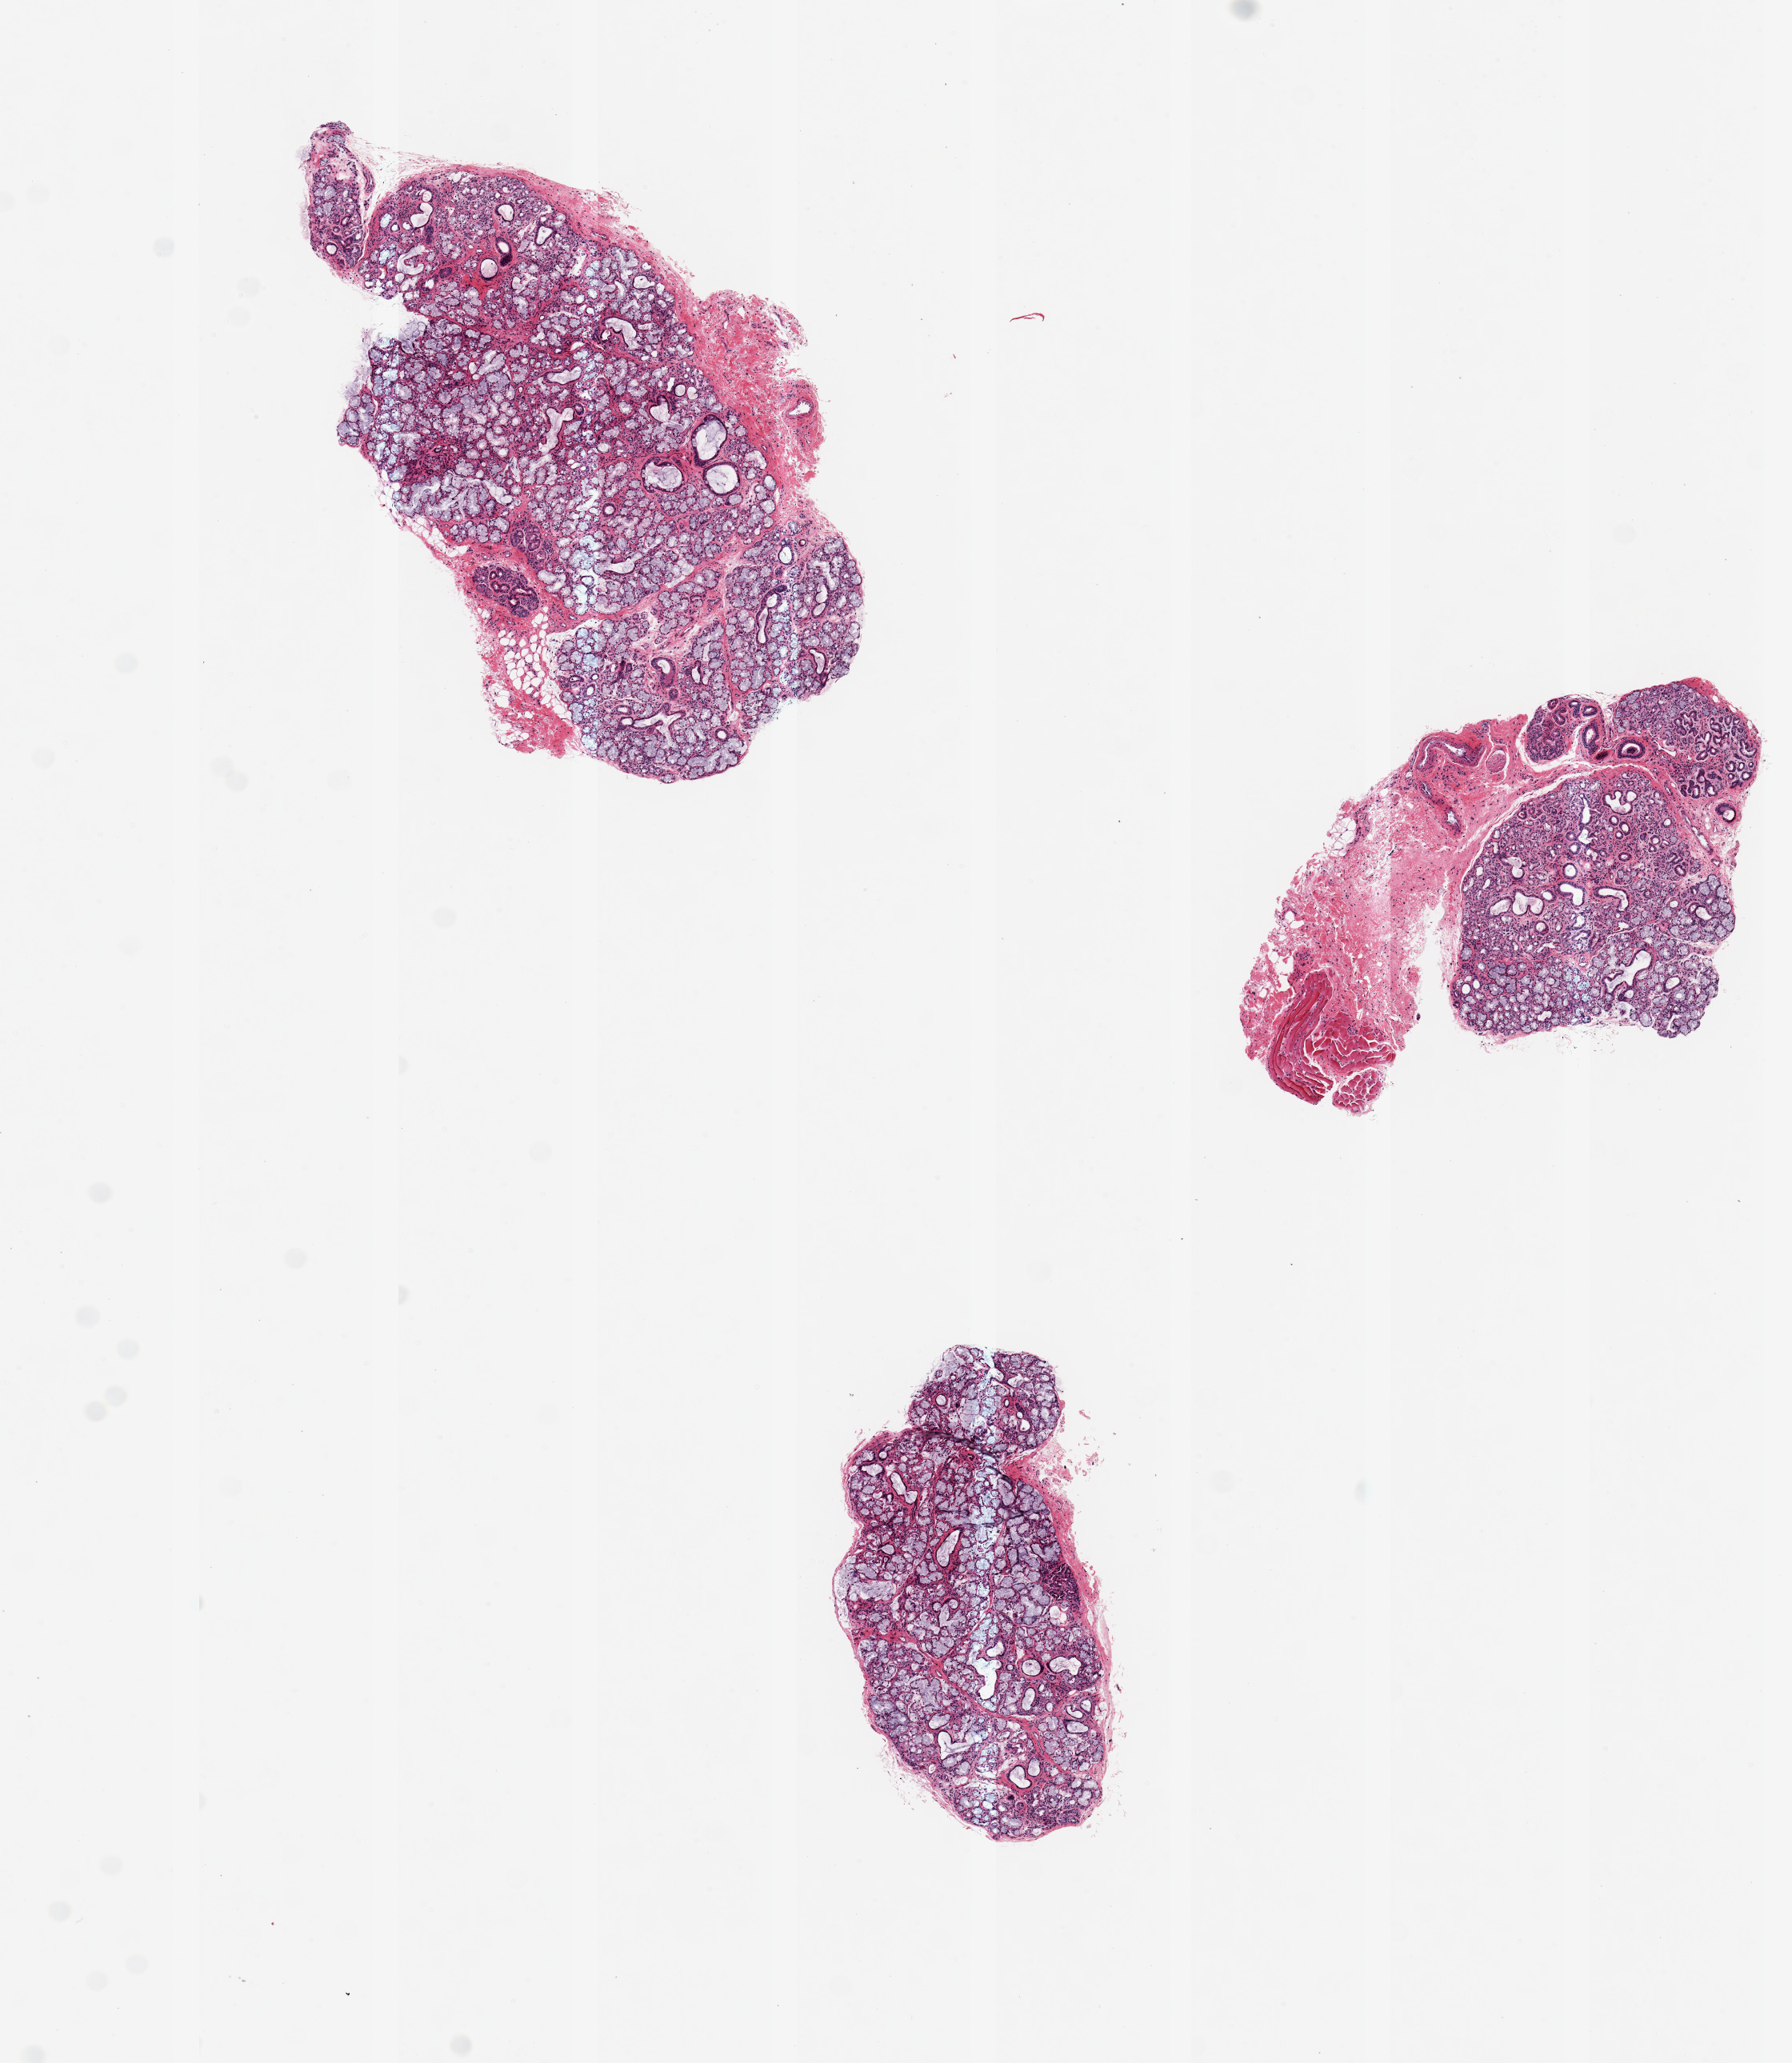
Haematoxylin and eosin whole-slide image, whole scanned area (about 8.9 x 10.2 mm) shown as a low-resolution overview; PAXgene-fixed paraffin-embedded (PFPE) section; section of minor salivary gland (target tissue); tissue donor sample. Male donor.
Review note (as recorded): 3 pieces, well preserved ~2.5mm d., one with ~2.5mm adherent fibrous nubbin.